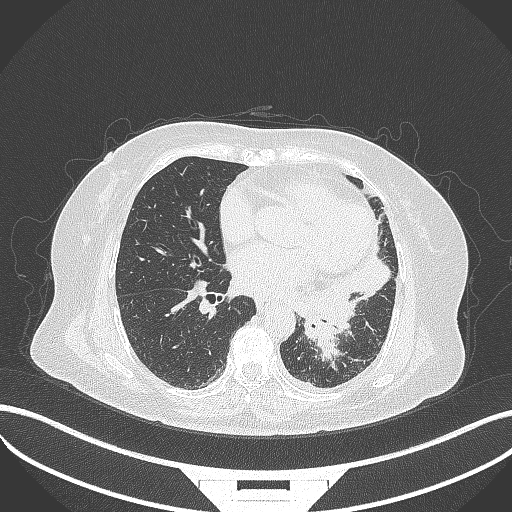
Chest CT, one axial slice. Slice 156 of 322 in the series (ordered by position). Reconstruction kernel B70f. Lung window (W 1500 / L -600 HU). 1 mm slice thickness. 512 × 512 image matrix, field of view 400 × 400 mm. Female patient, age 69 years. Case-level facts recorded for this patient, not image findings: clinical TNM (as recorded): T2b N3 M1.
Structures marked on this image (rectangle marked by the reading radiologist):
- lung tumour (recorded histology: adenocarcinoma): bounding box <298,282,355,362> (left, top, right, bottom; pixels)